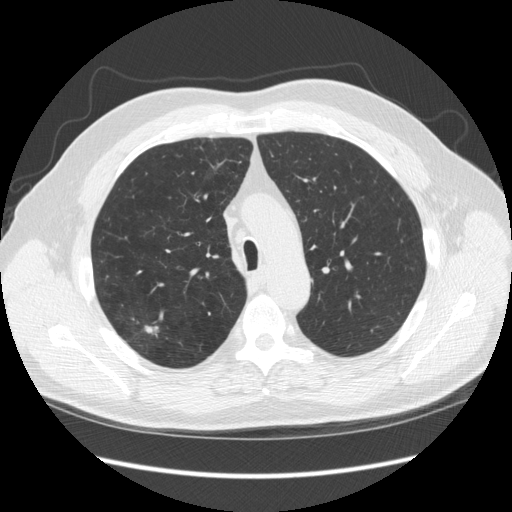
Low-dose screening chest CT, one axial slice. Slice 180 of 248 in the series (ordered by position). 120 kVp. Lung window (W 1500 / L -600 HU). 2.5 mm slice thickness. 512 × 512 image matrix, field of view 380 × 380 mm.
Outlined on this slice (outlined manually by an expert reader):
- lesion 1 (tumor, upper lobe of right lung): box from (x=144, y=325) to (x=154, y=334) px